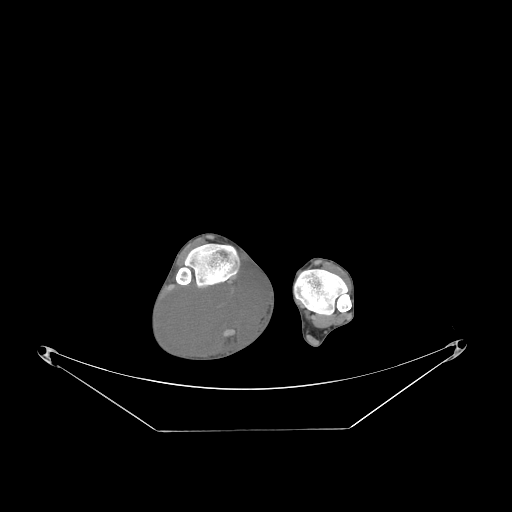
CT of an extremity soft-tissue mass (from a PET/CT study), one axial slice. Slice 51 of 267 in the series (ordered by position). 140 kVp. Soft-tissue window (W 400 / L 40 HU). 512 × 512 image matrix, field of view 500 × 500 mm. Male patient. From the clinical record (not read from this slice): histological type: liposarcoma - round cell; grade: high; site of the primary tumour: right calf.
Structures marked on this image (expert contour drawn on MRI and transferred to this co-registered scan by the dataset authors):
- gross tumour volume (mass): bounding box [x1, y1, x2, y2] px = [162, 274, 268, 359]